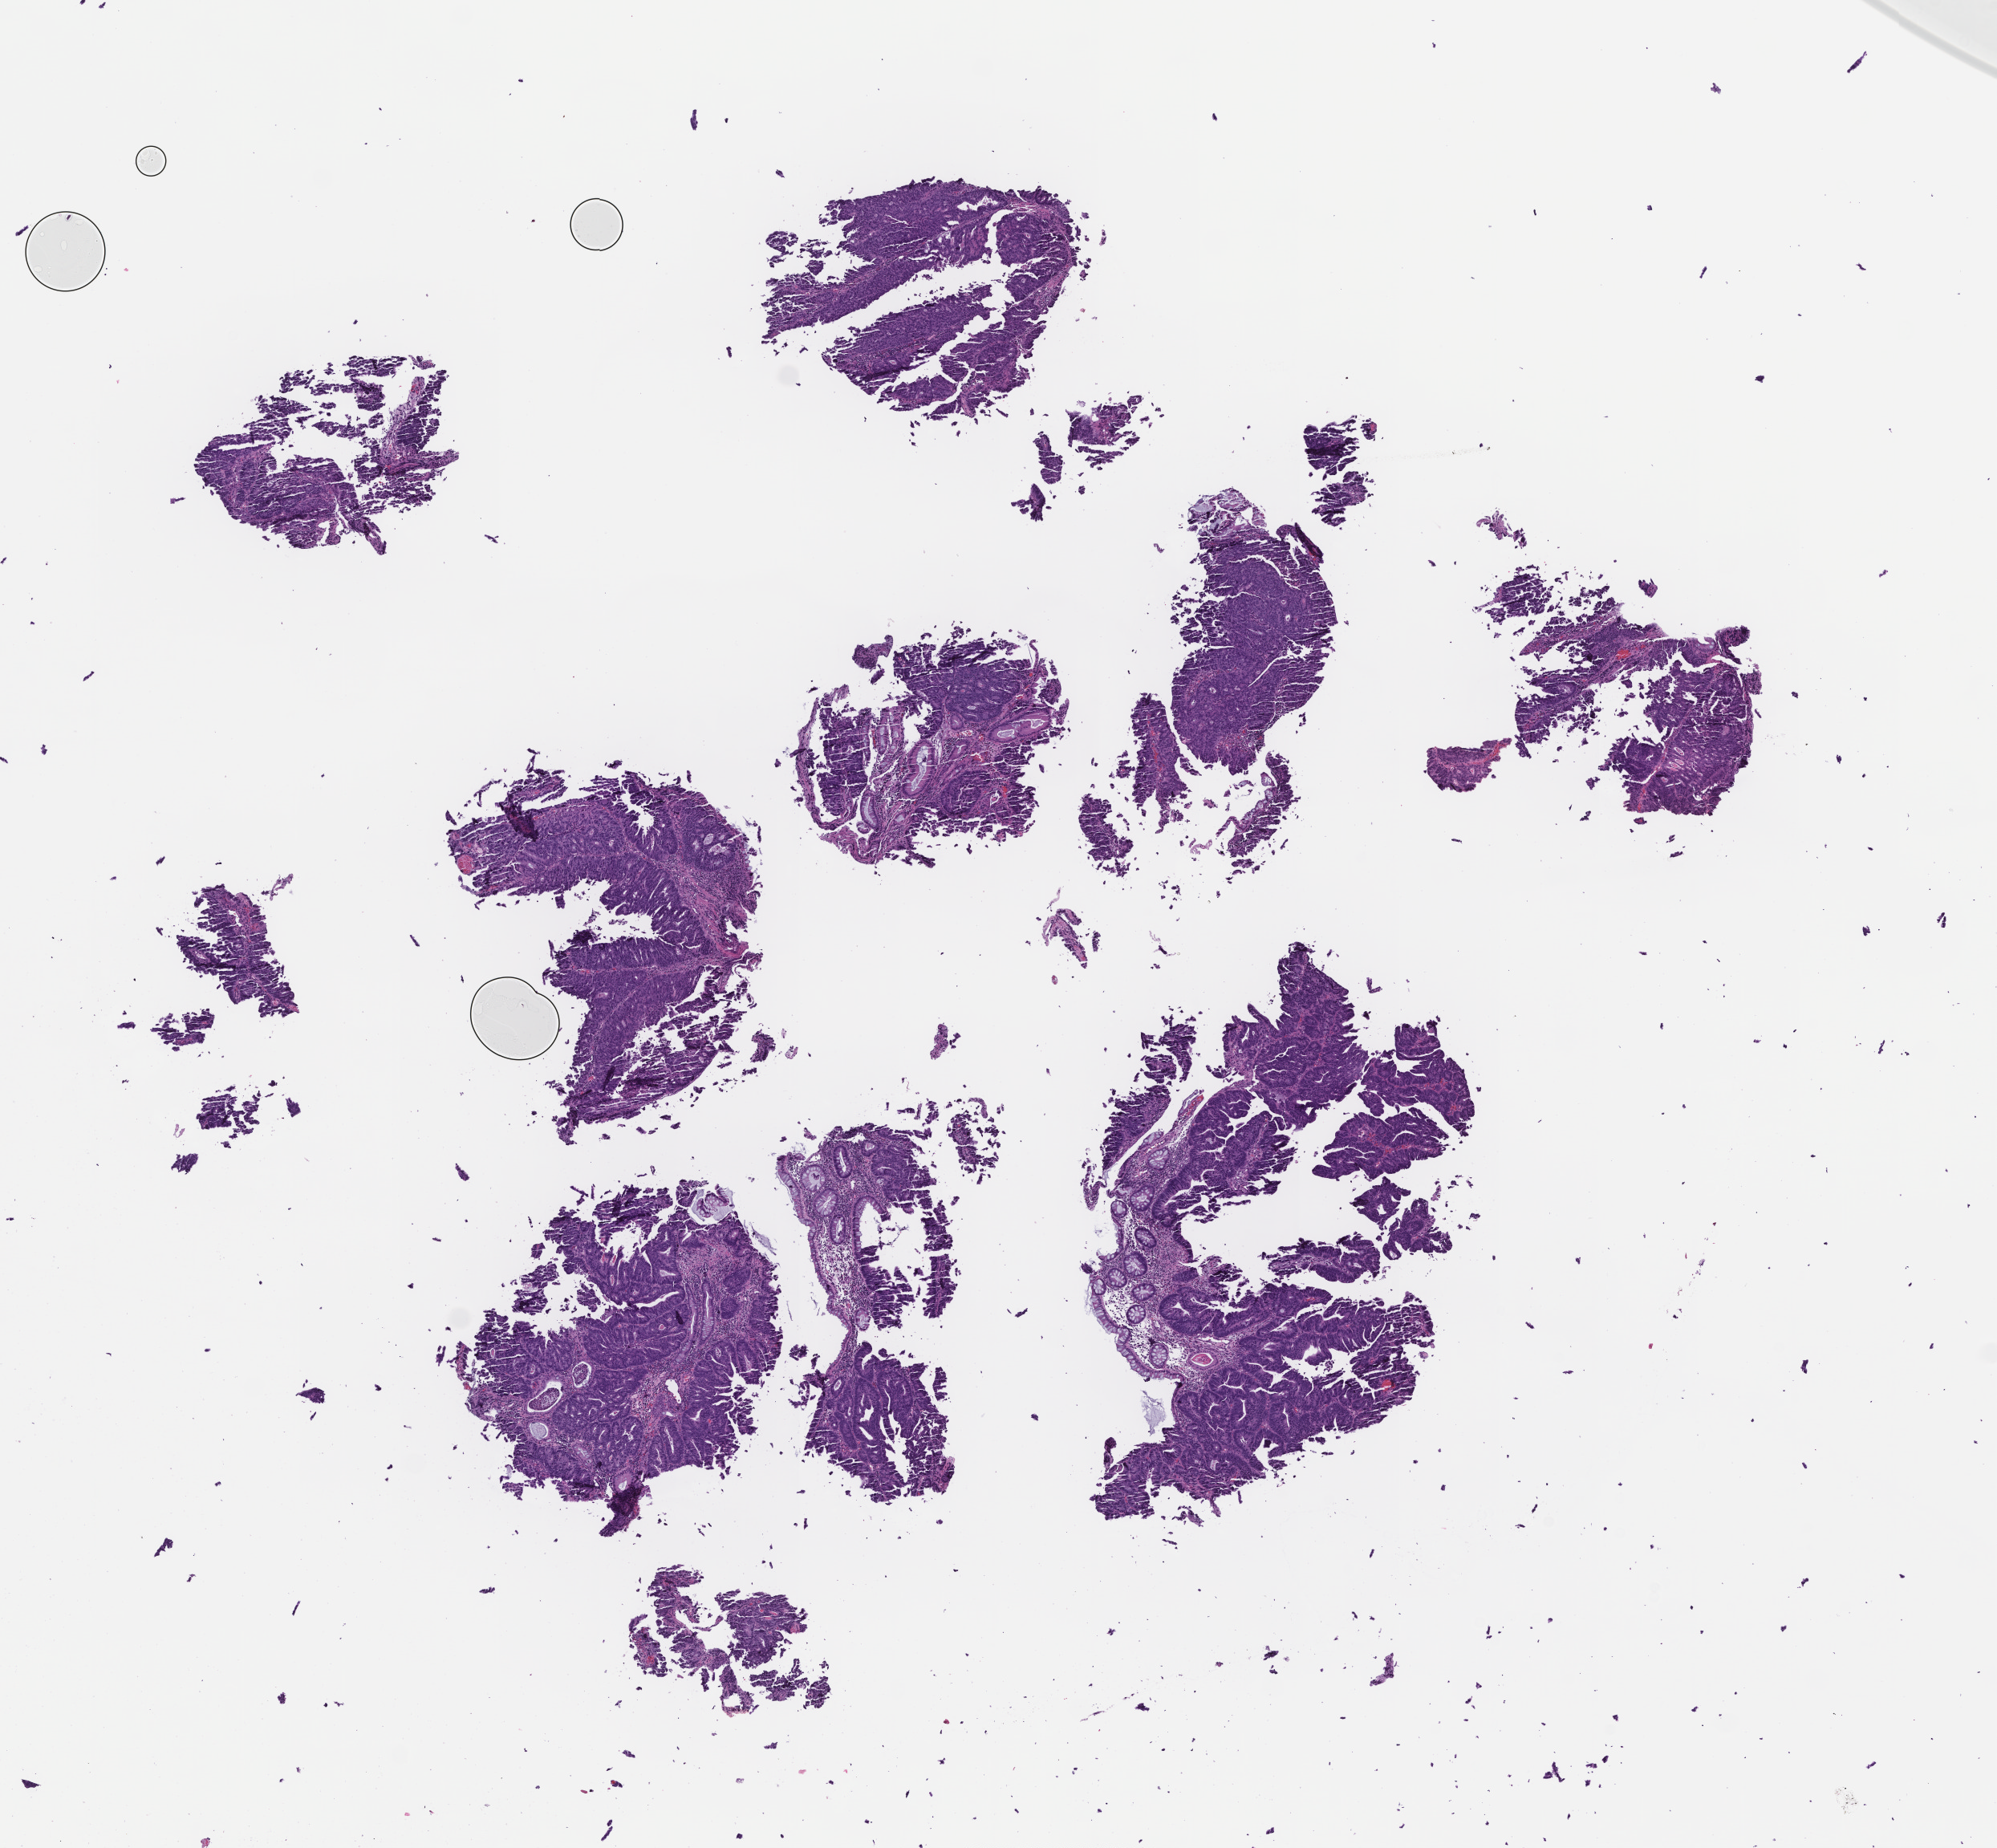
Whole-slide image, H&E stain, whole scanned area (about 10.1 x 9.3 mm) shown as a low-resolution overview. Formalin-fixed, paraffin-embedded (FFPE) tissue. Site: colon. Archival tissue. Patient sex: male.
- this section: primary tumour tissue
- diagnosis: Colorectal Carcinoma